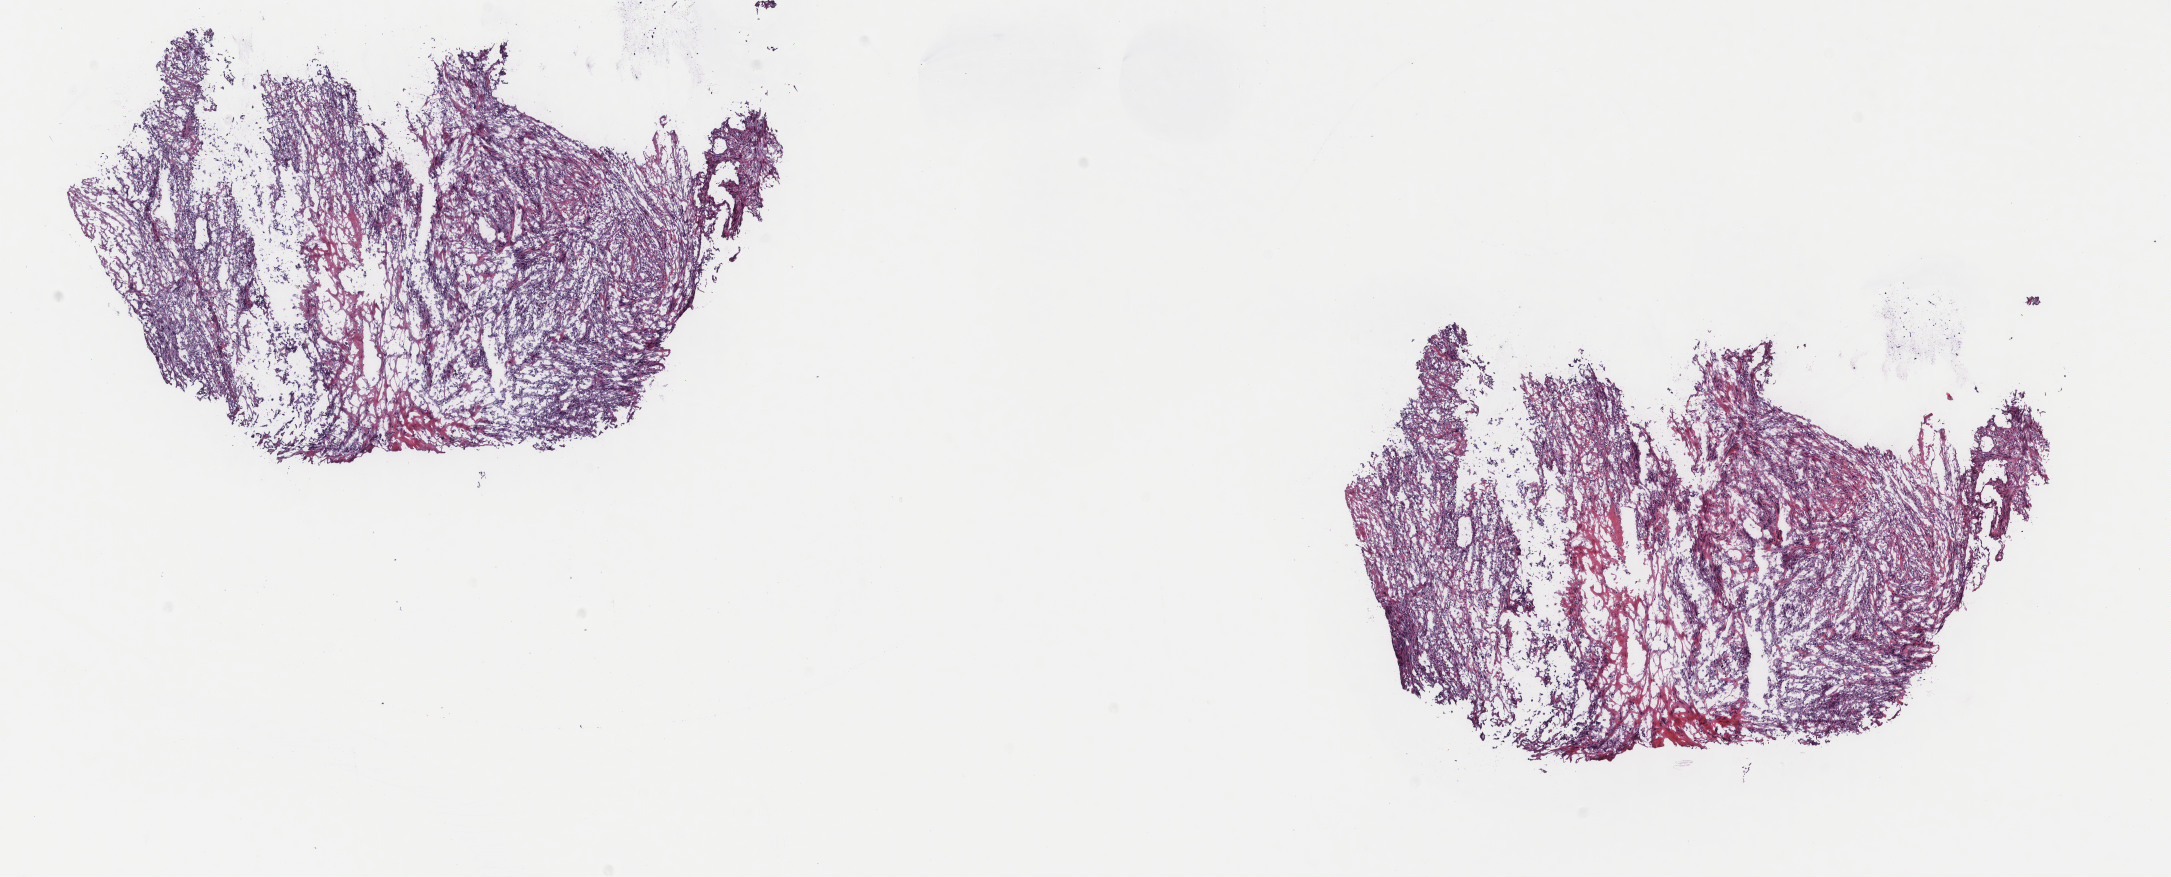
Whole-slide histology image, H&E — whole scanned area (about 17.2 x 7.0 mm, from a 40x scan) shown as a low-resolution overview, frozen section from the top of the tissue portion, primary tumour sample from the connective, subcutaneous and other soft tissues. Female patient; age at initial diagnosis 63 years. Composition of this section per pathologist review: tumour cells 80%, tumour nuclei 100%, normal cells 0%, stromal cells 20%, necrosis 0%. Inflammatory infiltration, as recorded: lymphocyte infiltration 0%, monocyte infiltration 2%, neutrophil infiltration 0%.
• diagnosis: Leiomyosarcoma, NOS (connective, subcutaneous and other soft tissues, NOS)